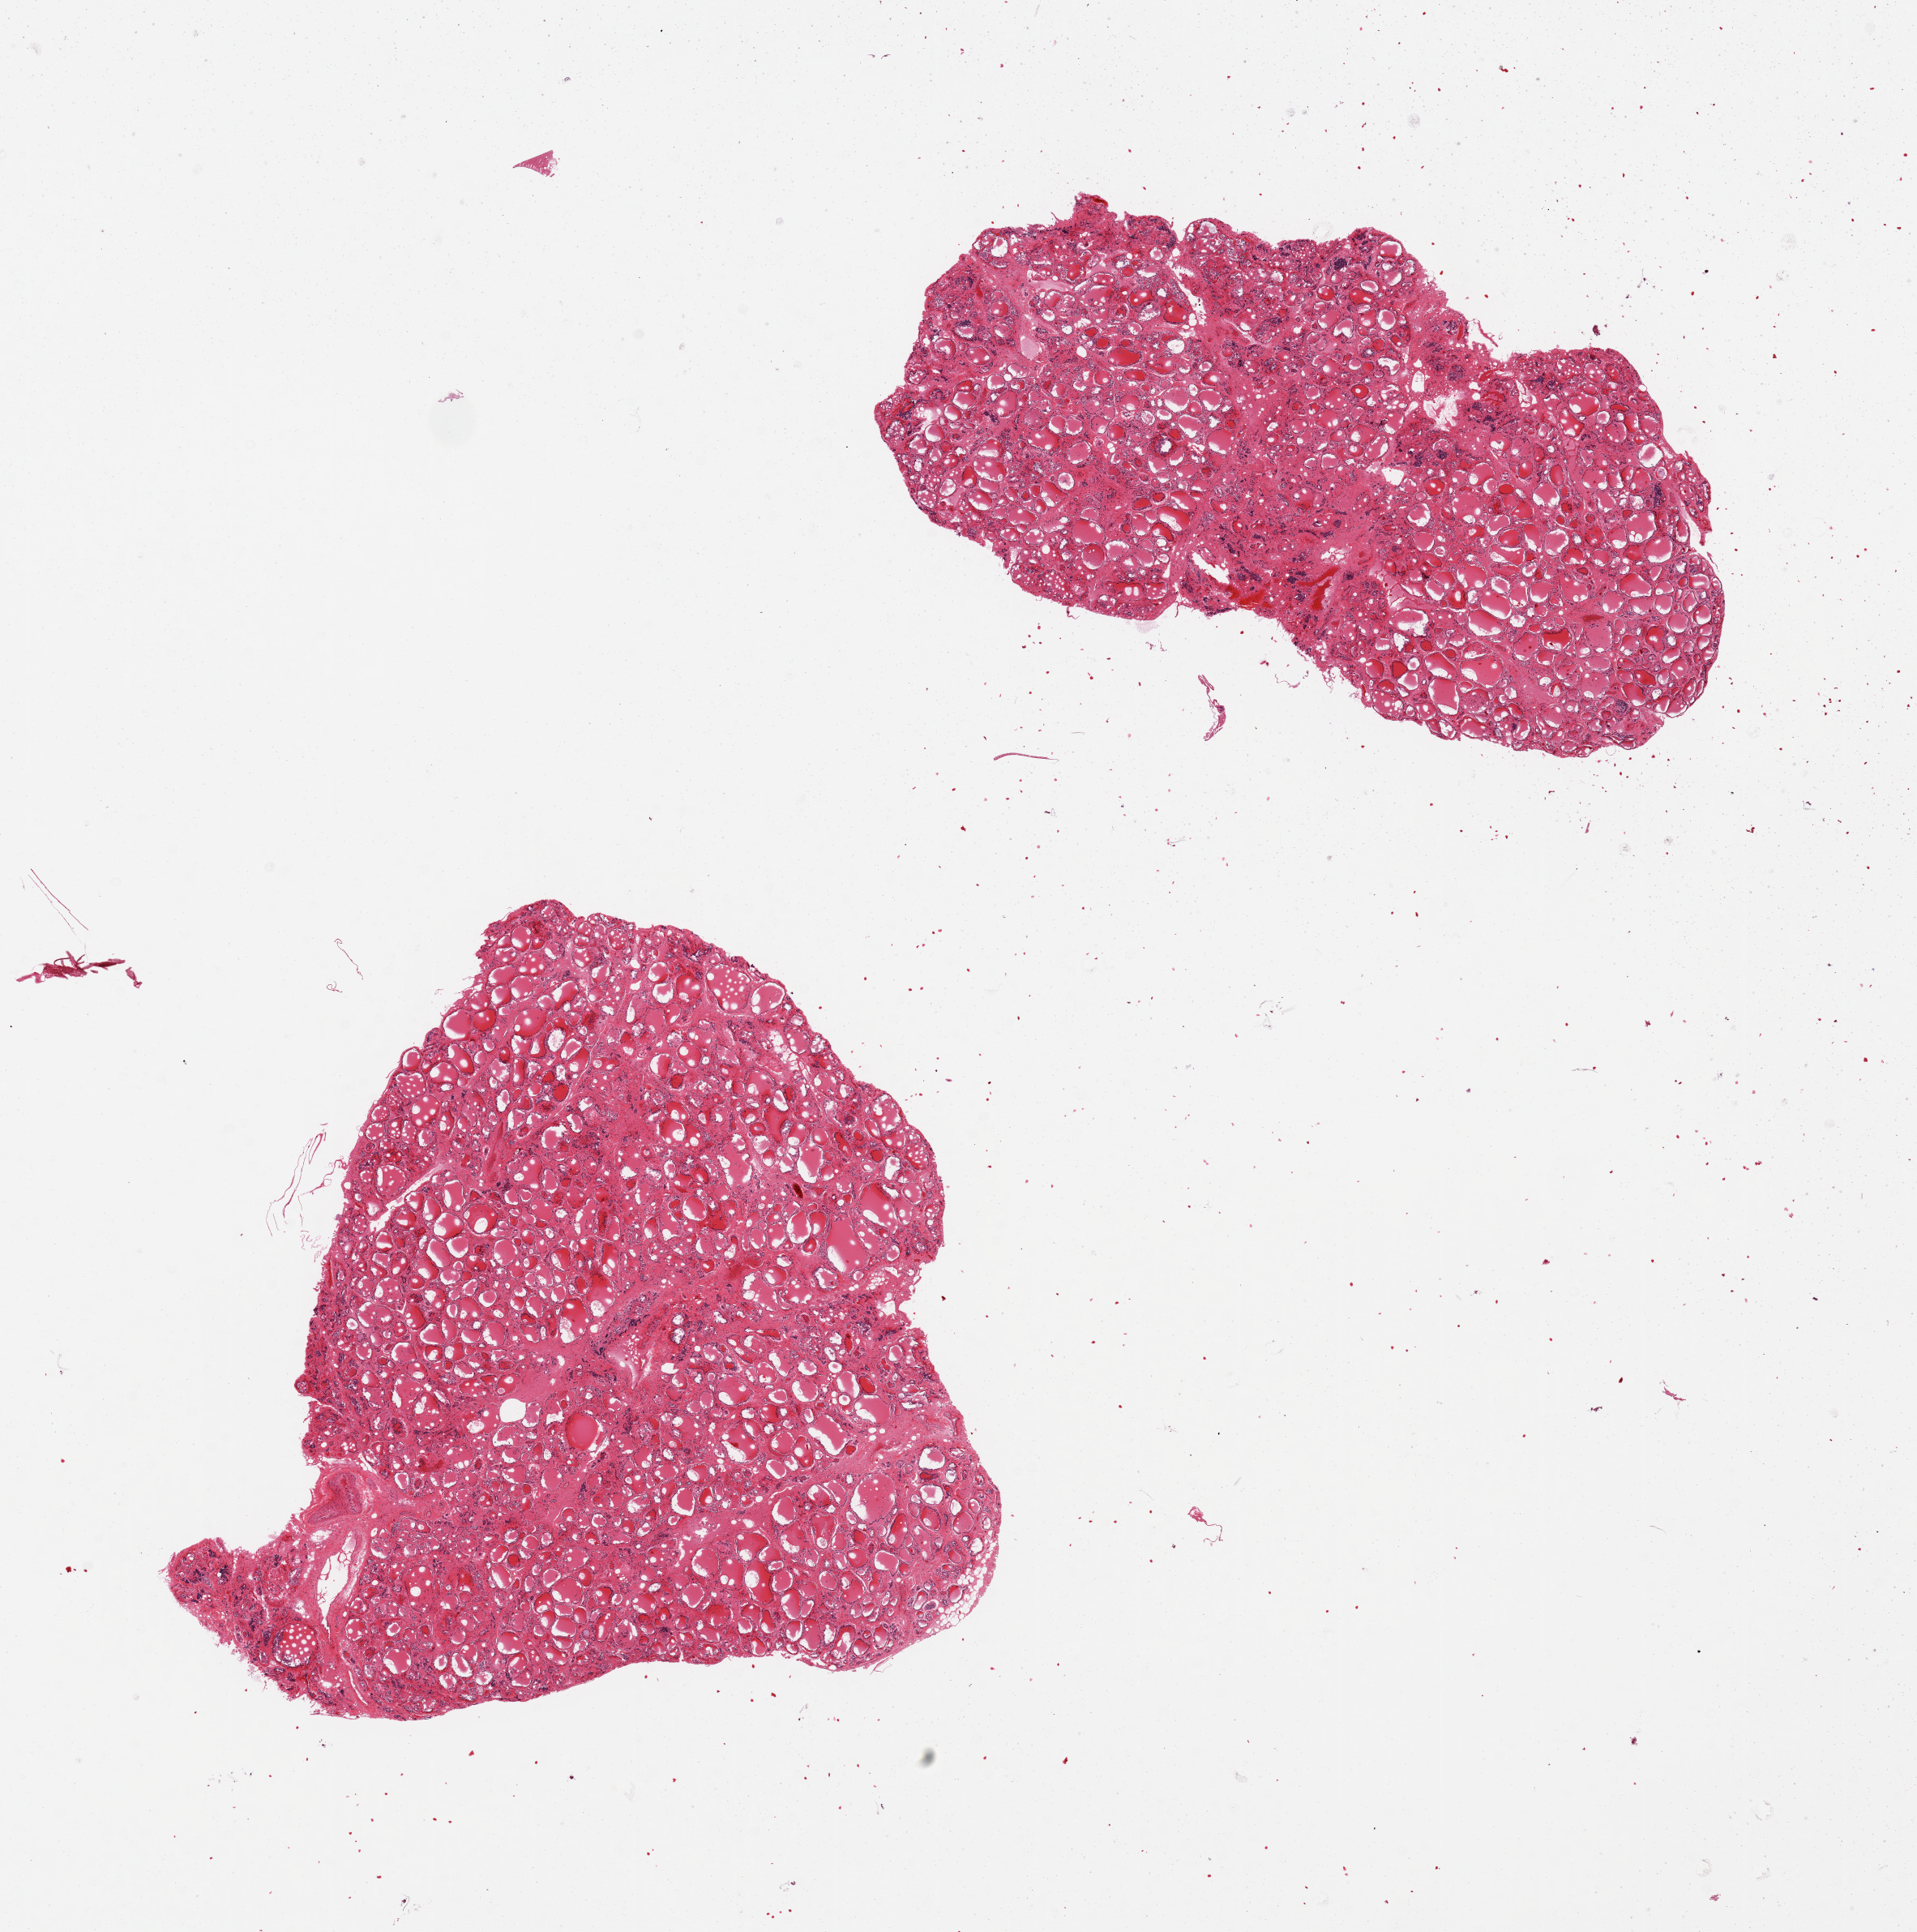
Digitized H&E-stained section — whole scanned area (about 18.7 x 18.8 mm, from a 20x scan) shown as a low-resolution overview. PAXgene-fixed, paraffin-embedded tissue. Target tissue: thyroid. Tissue donor sample. Female donor.
• review note (as recorded): 2 pieces, regressive changes